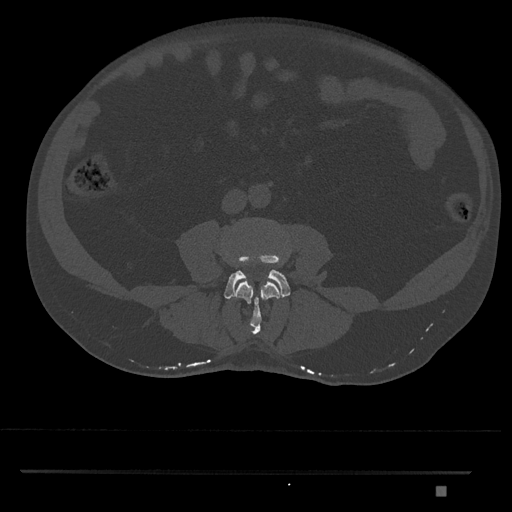
CT including the spine, one axial slice. Slice 648 of 1134 in the series (ordered by position). Reconstruction kernel Br40s/3. 120 kVp. Bone window (W 1800 / L 400 HU). 0.5 mm slice thickness. 512 × 512 image matrix. Patient: male, 65 years. From the clinical record (not read from this slice): primary cancer: prostate.
Outlined on this slice (semi-automatically segmented with operator editing):
- L3 vertebra: box from (x=234, y=281) to (x=280, y=335) px
- L4 vertebra: (x=224, y=244)–(x=291, y=299)